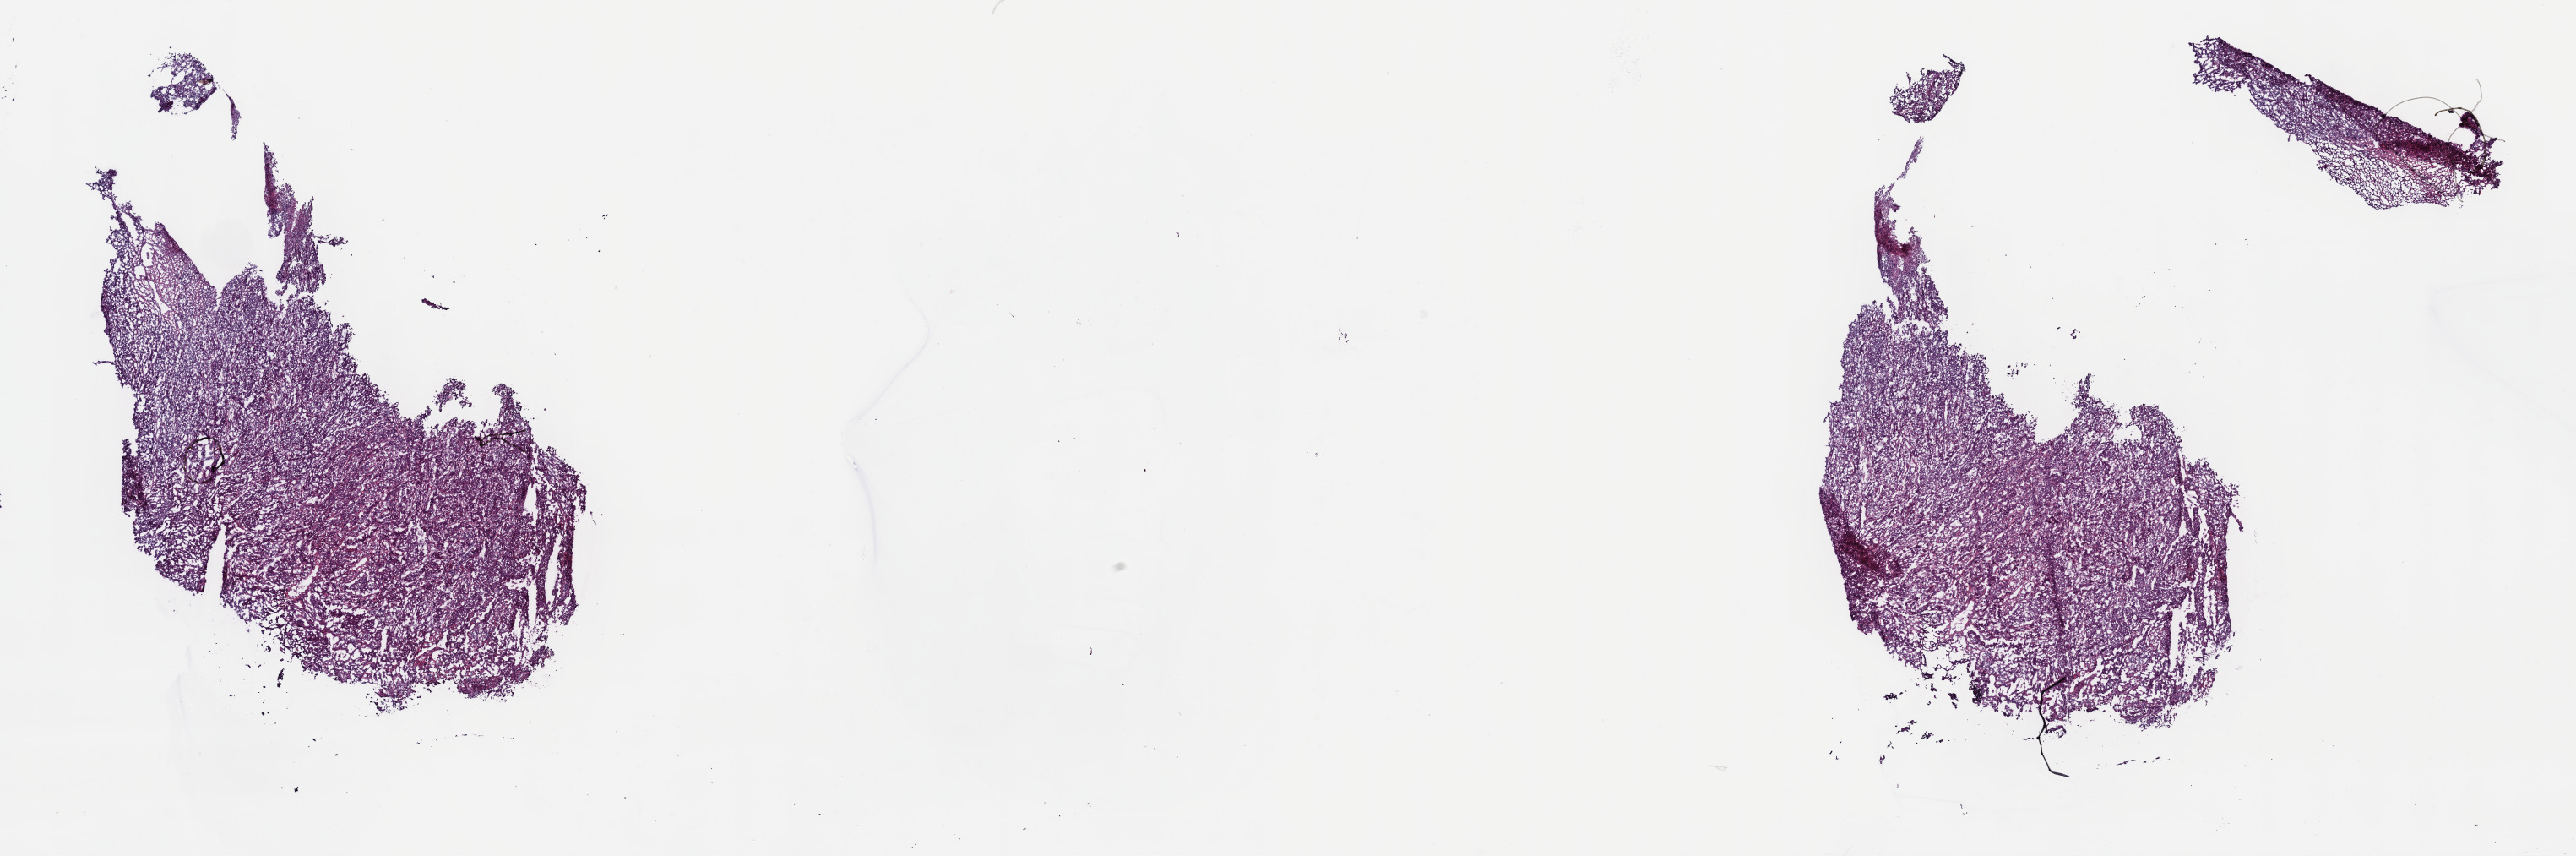
Whole-slide histology image, Hematoxylin and eosin (H&E) stained — low-resolution overview of the scanned area, about 24.7 x 8.2 mm. Frozen section from the top of the tissue portion. Sample: primary tumour, bladder. Patient: male, age at initial diagnosis 80 years. Histologic grade: high grade. Pathologist review of this section (percent, as recorded): tumour cells 100%, tumour nuclei 75%, normal cells 0%, stromal cells 0%, necrosis 0%. Inflammatory infiltration, as recorded: lymphocyte infiltration 2%, monocyte infiltration 0%, neutrophil infiltration 0%.
* AJCC pathologic stage: II (7th edition)
* pathologic diagnosis: Papillary transitional cell carcinoma (posterior wall of bladder)
* lymph nodes positive (case pathology): 0 of 6 examined
* TNM: T2b N0 M0